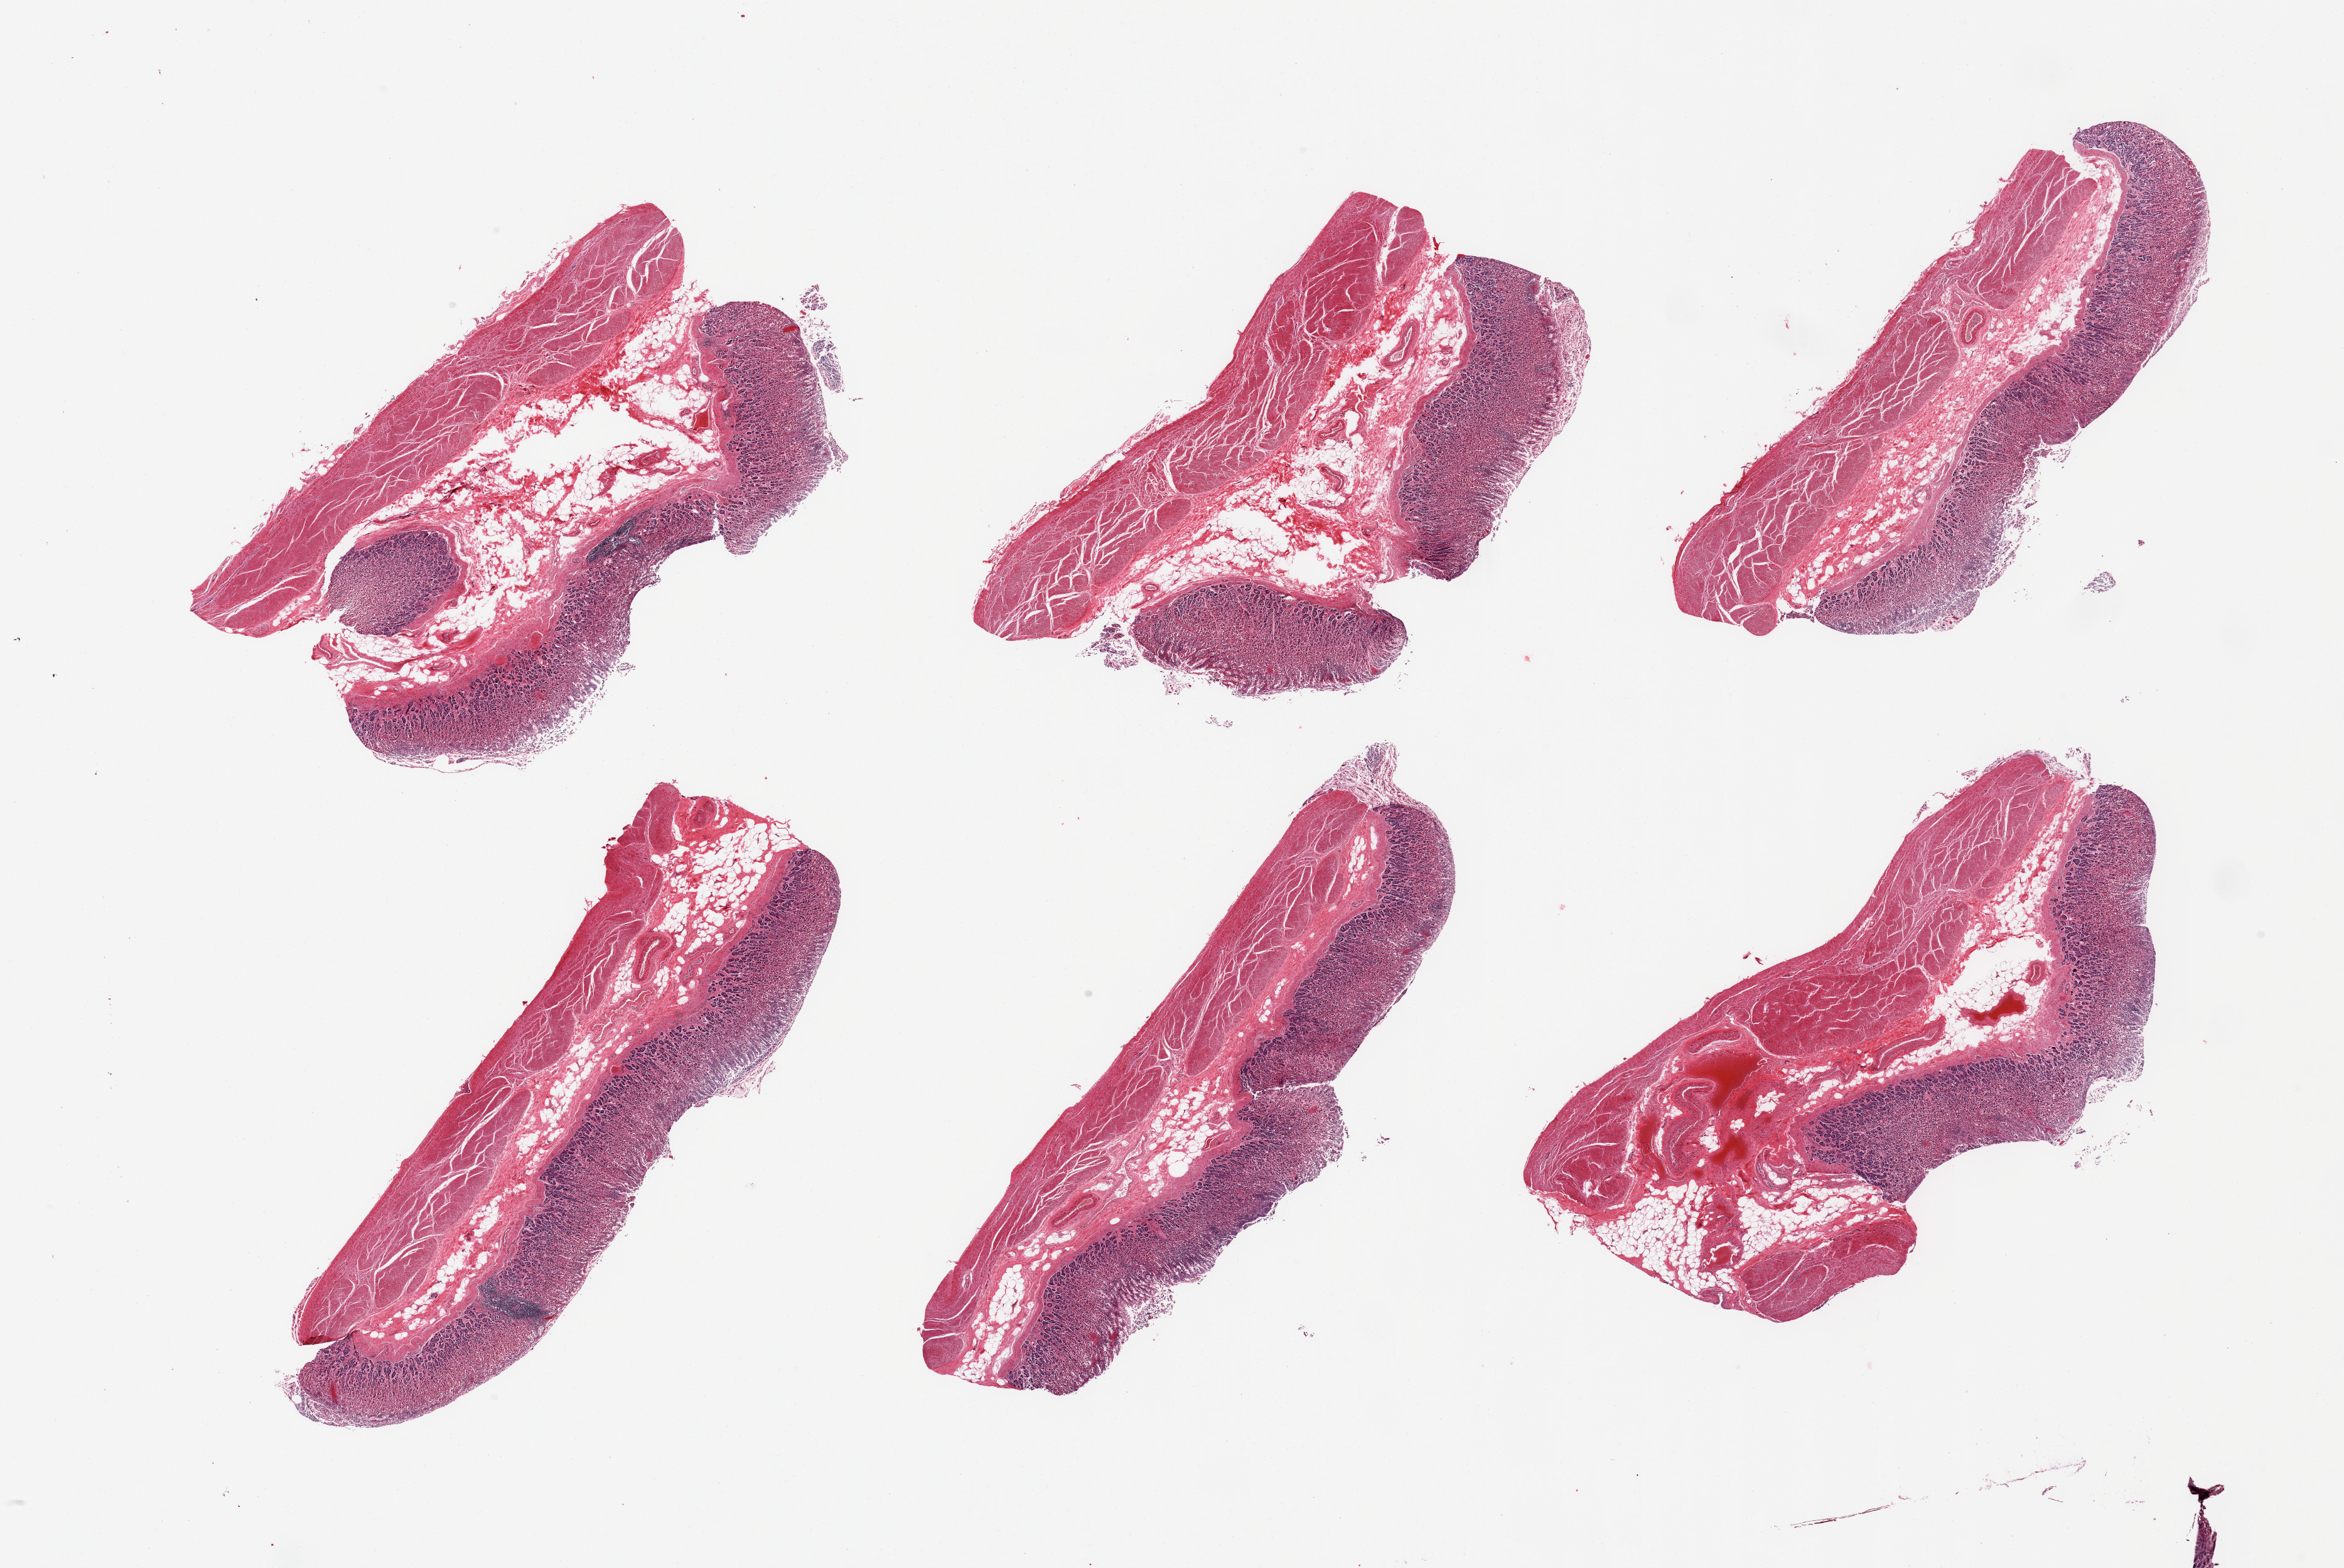
Haematoxylin and eosin whole-slide image — whole scanned area (about 29.5 x 19.8 mm, from a 20x scan) shown as a low-resolution overview; PAXgene-fixed, paraffin-embedded tissue; sampled site (target tissue): stomach; tissue donor sample.
- pathologist's review note for this sample: 6 pieces, mucosa up to ~1mm, ~40% thickness, moderately advanced autolysis